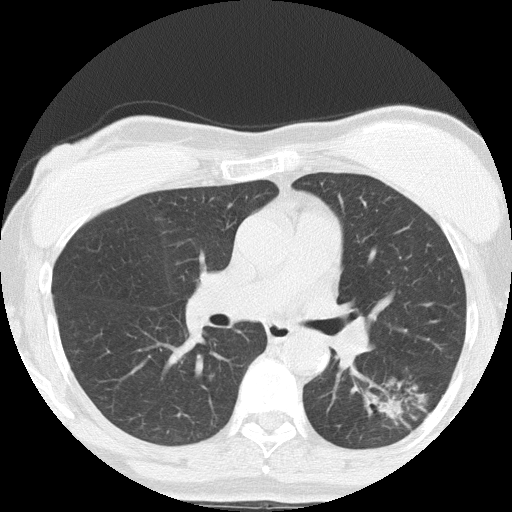
Low-dose screening chest CT, one axial slice. Slice 86 of 152 in the series (ordered by position). Reconstruction kernel FC51. 120 kVp. Lung window (W 1500 / L -600 HU). 2 mm slice thickness. 512 × 512 image matrix, field of view 308 × 308 mm.
Structures marked on this image (expert manual segmentation):
- lesion 1 (tumor, lower lobe of left lung): box from (x=382, y=398) to (x=402, y=418) px